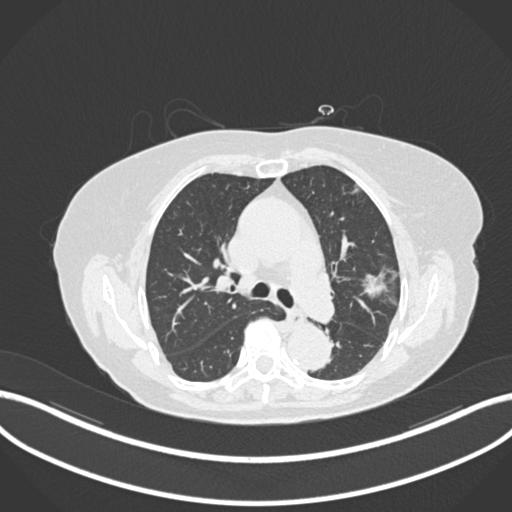
Chest CT, one axial slice; slice 102 of 168 in the series (ordered by position); reconstruction kernel B30f; lung window (W 1500 / L -600 HU); 1 mm slice thickness; 512 × 512 image matrix, field of view 400 × 400 mm. Female patient, age 75 years. From the clinical record (not read from this slice): clinical TNM (as recorded): T1c N0 M0.
Annotated regions visible in this slice (bounding box drawn by a radiologist):
- lung tumour (recorded histology: adenocarcinoma): bounding box (x1, y1, x2, y2) in pixels: (362, 266, 387, 296)